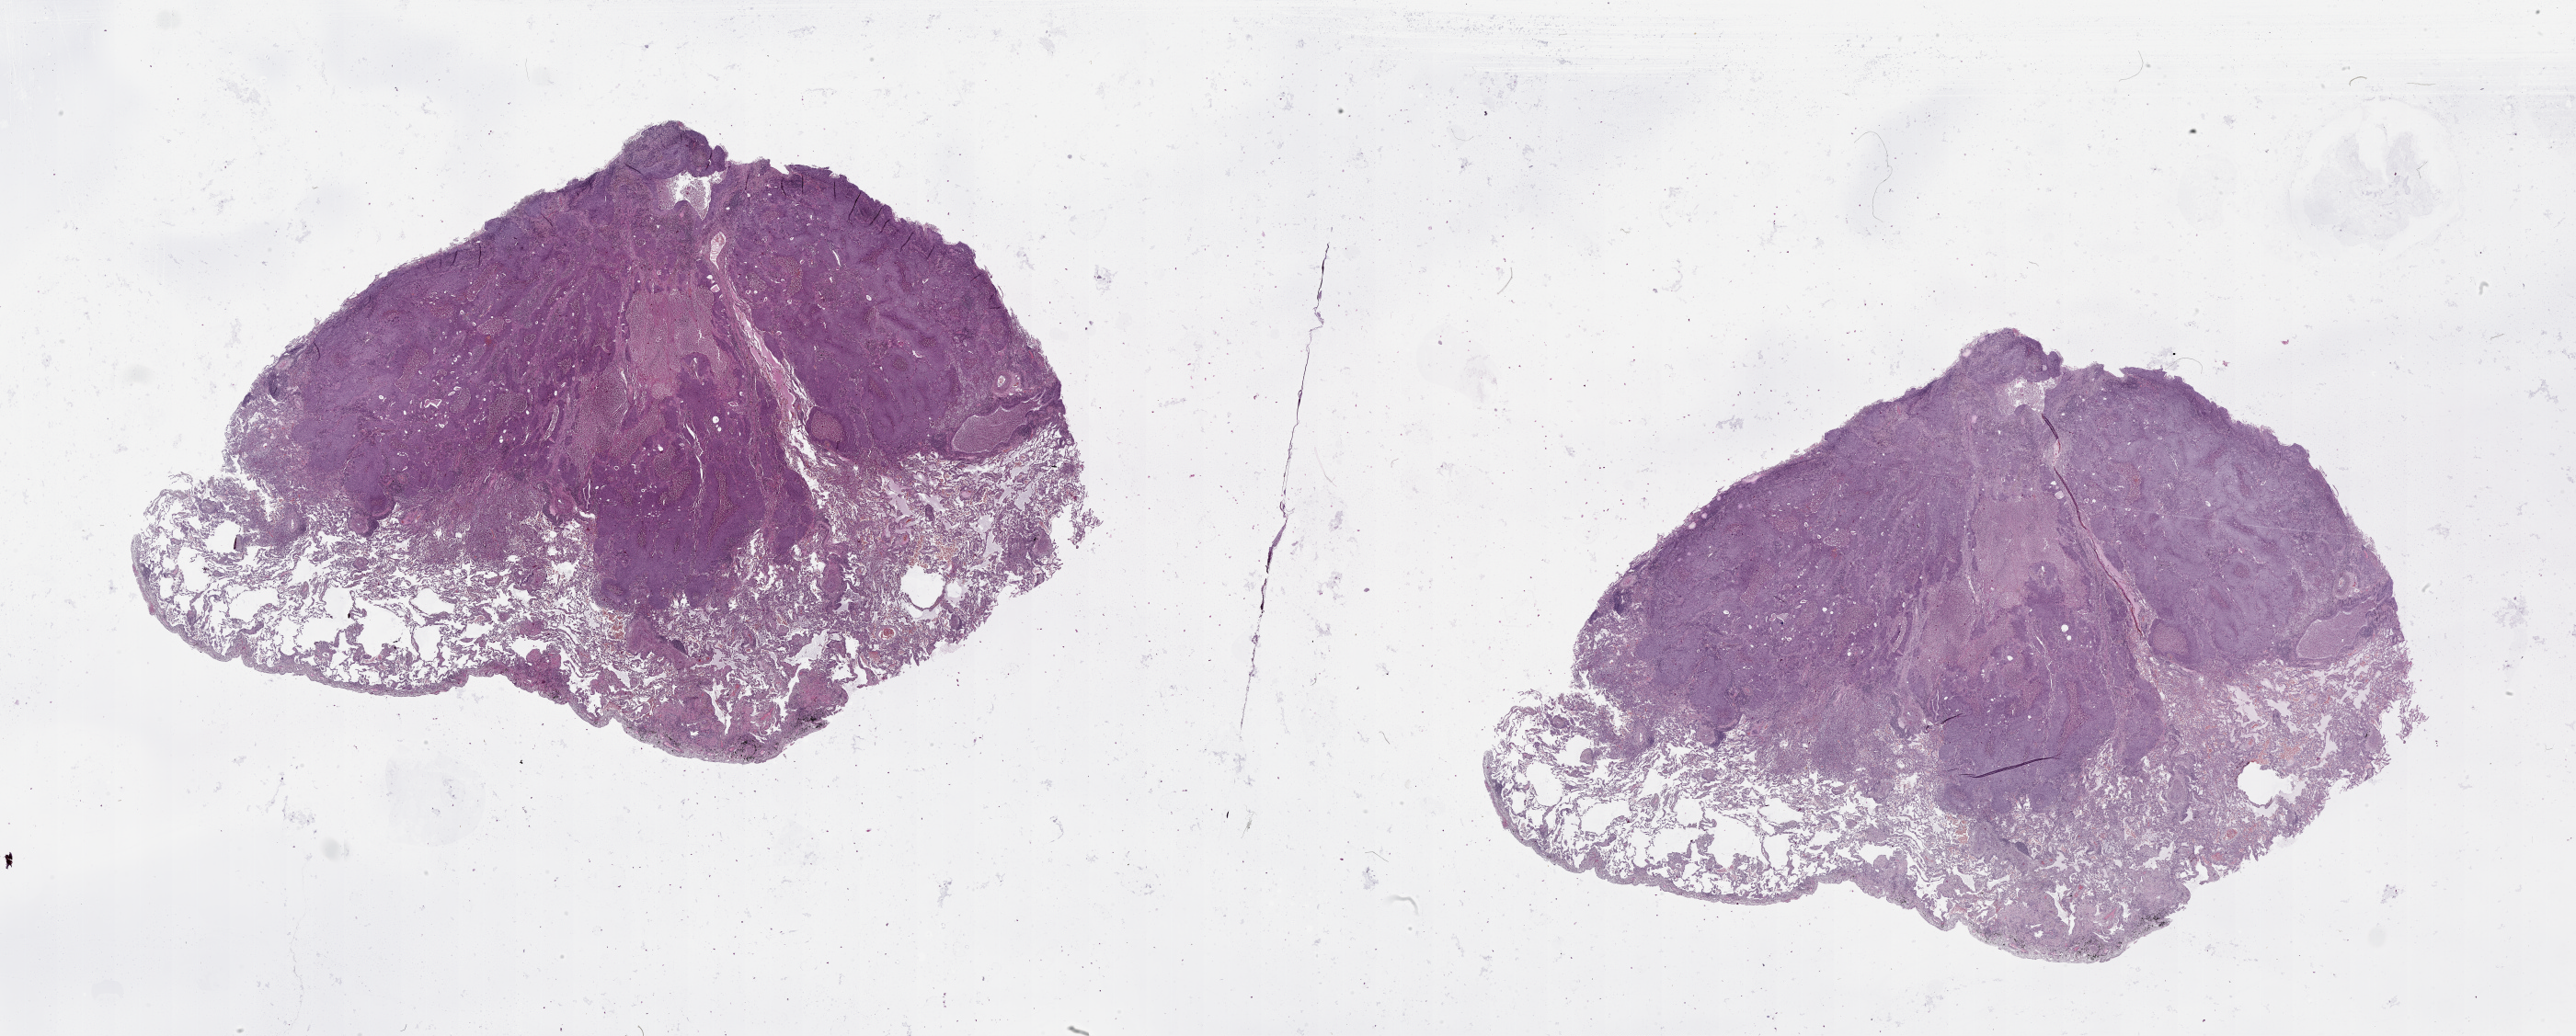
Digitized H&E tissue section (whole slide), a low-resolution overview of the entire scanned area, about 45.1 x 18.1 mm. Lung, tumour tissue. Patient: male, age 75 years.
Patient diagnosis (cohort enrolment): squamous cell carcinoma (lung).